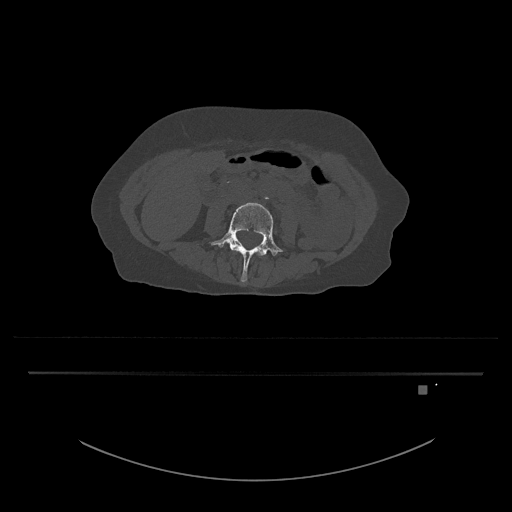
CT including the spine, one axial slice. Slice 367 of 797 in the series (ordered by position). 120 kVp. Bone window (W 1800 / L 400 HU). 0.5 mm slice thickness. 512 × 512 image matrix, field of view 500 × 500 mm. Patient: female, 57 years. Case-level facts recorded for this patient, not image findings: primary cancer: cervical.
Annotated regions visible in this slice (semi-automatic segmentation, software-assisted and operator-edited):
- L3 vertebra: bounding box [x1, y1, x2, y2] px = [258, 254, 262, 256]
- L4 vertebra: [209, 202, 283, 282]